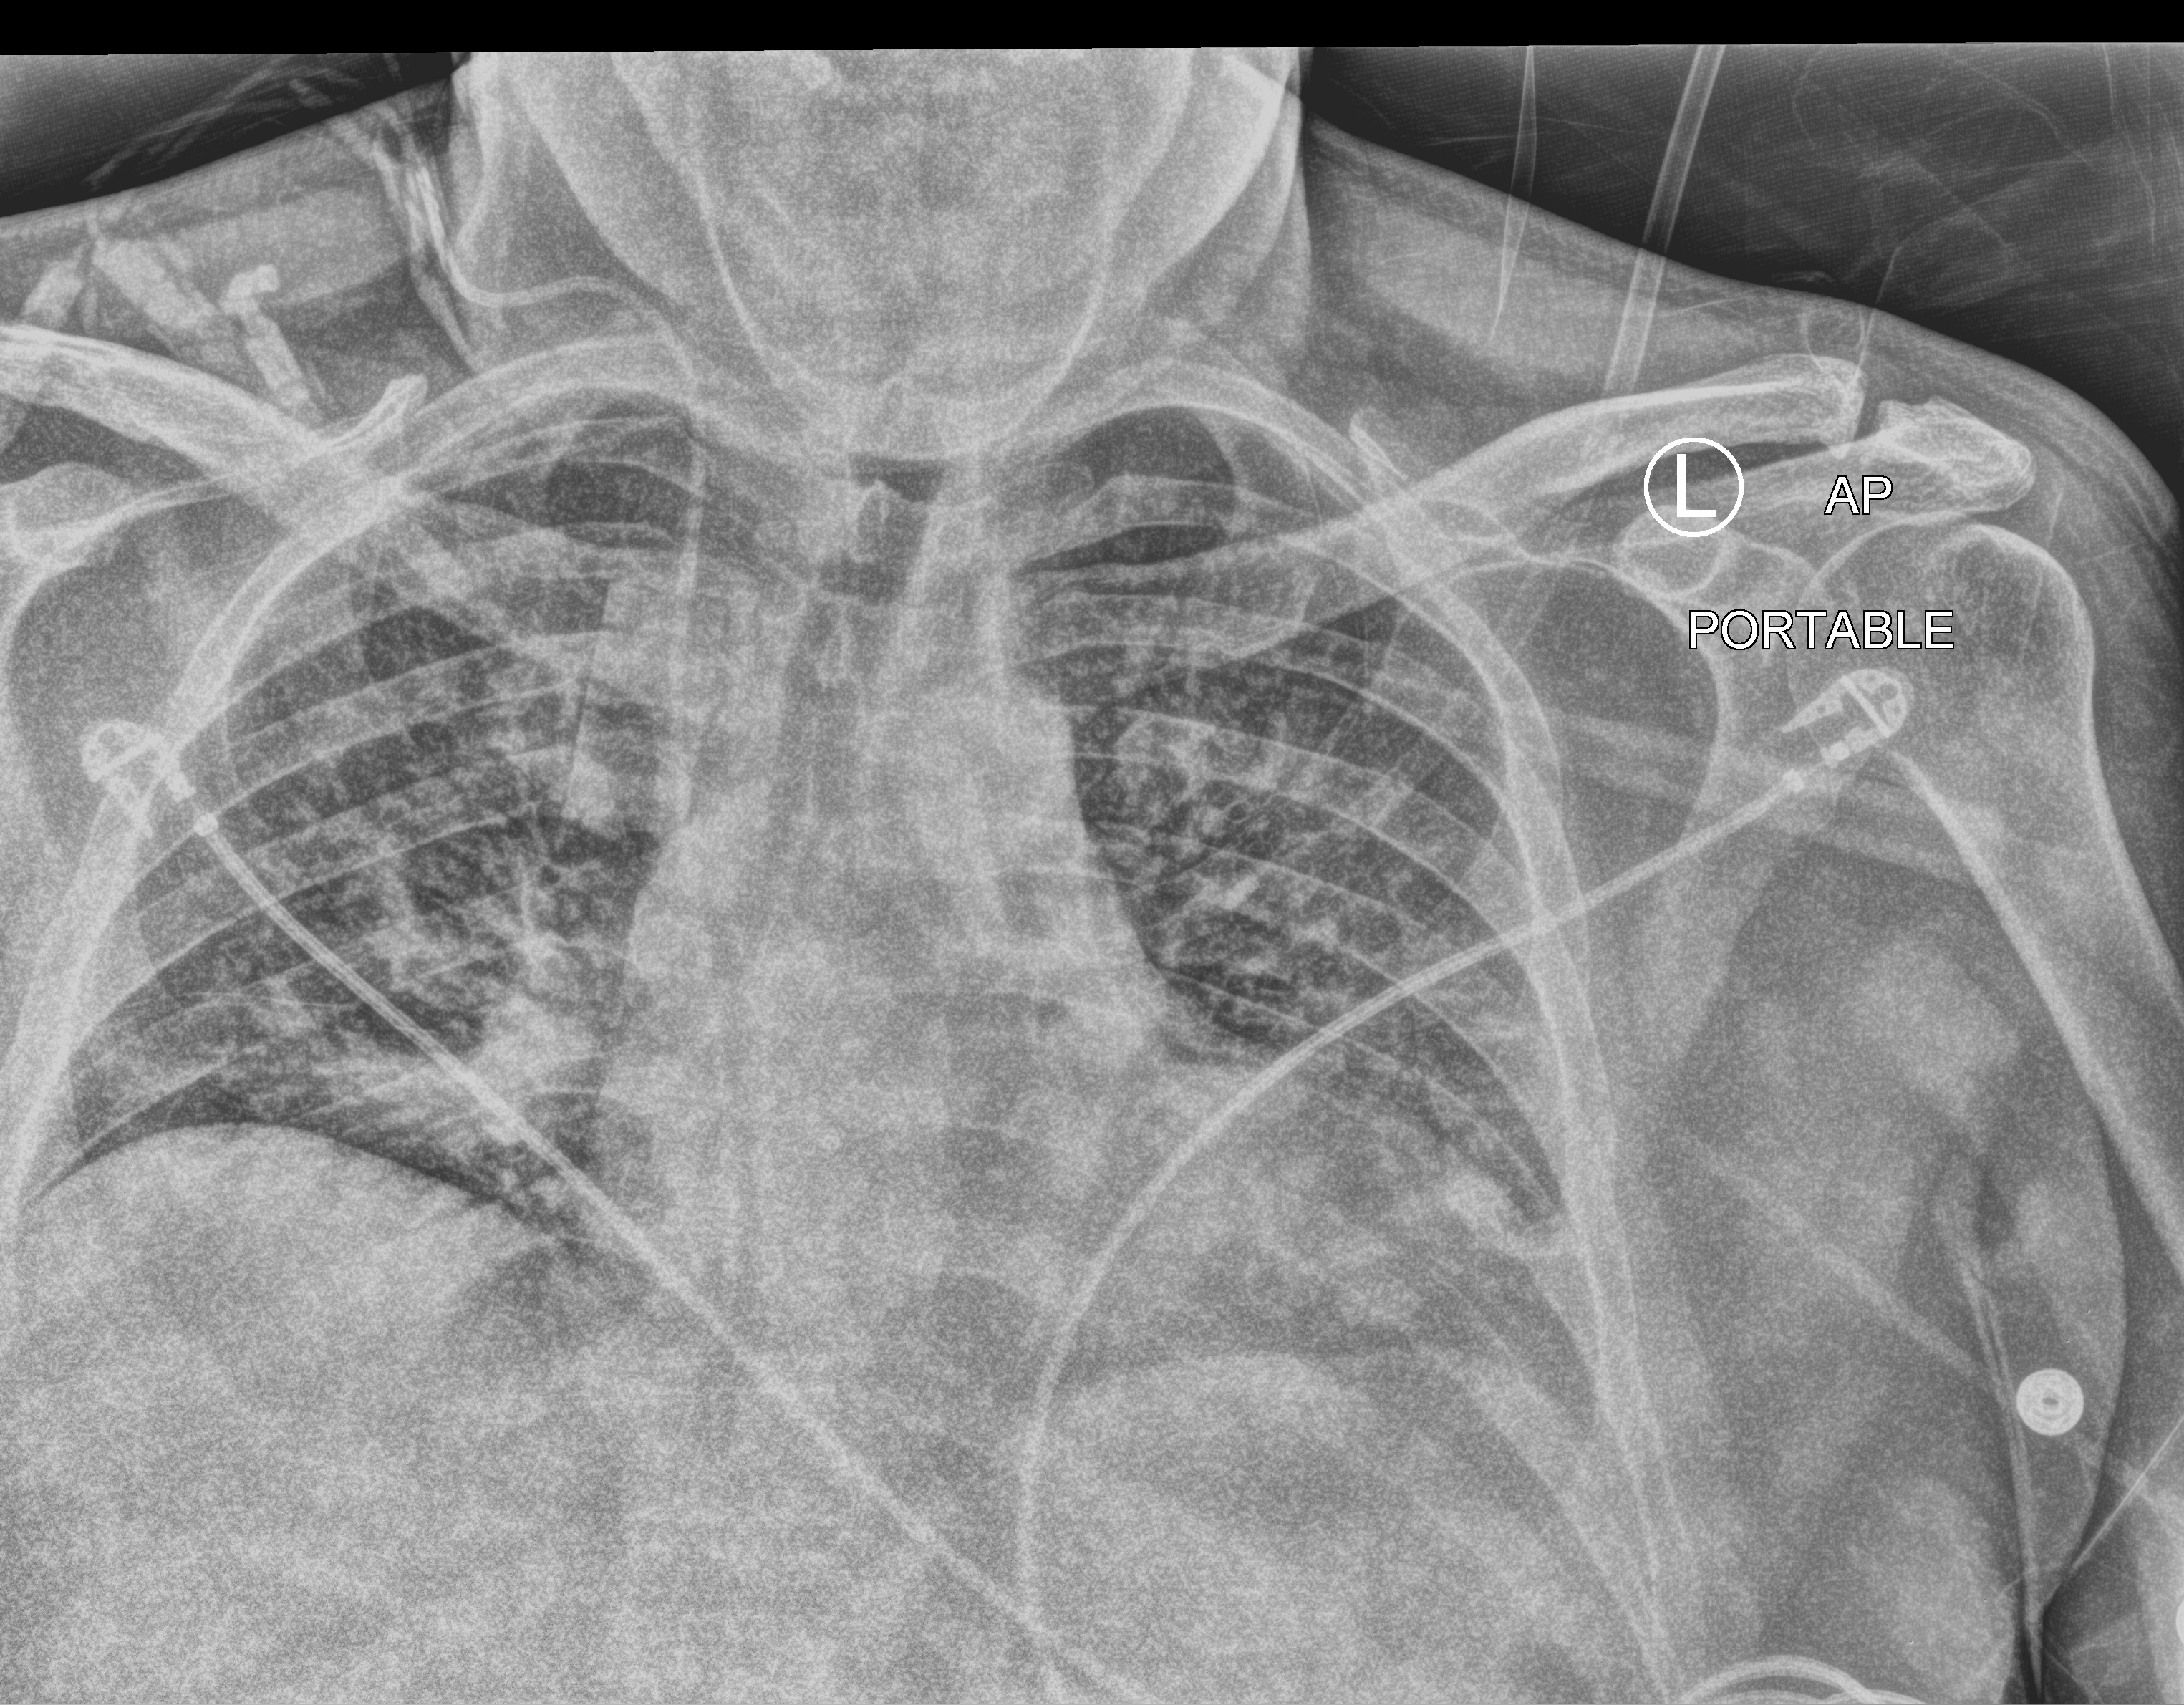
Chest X-ray (portable); anteroposterior (AP) projection. Male patient hospitalised with COVID-19, age 18–59 years.
From the hospital-stay record, not from the radiograph (when in the stay this image was taken is not recorded): mechanically ventilated during this hospital stay: yes; length of hospital stay: 17 days.